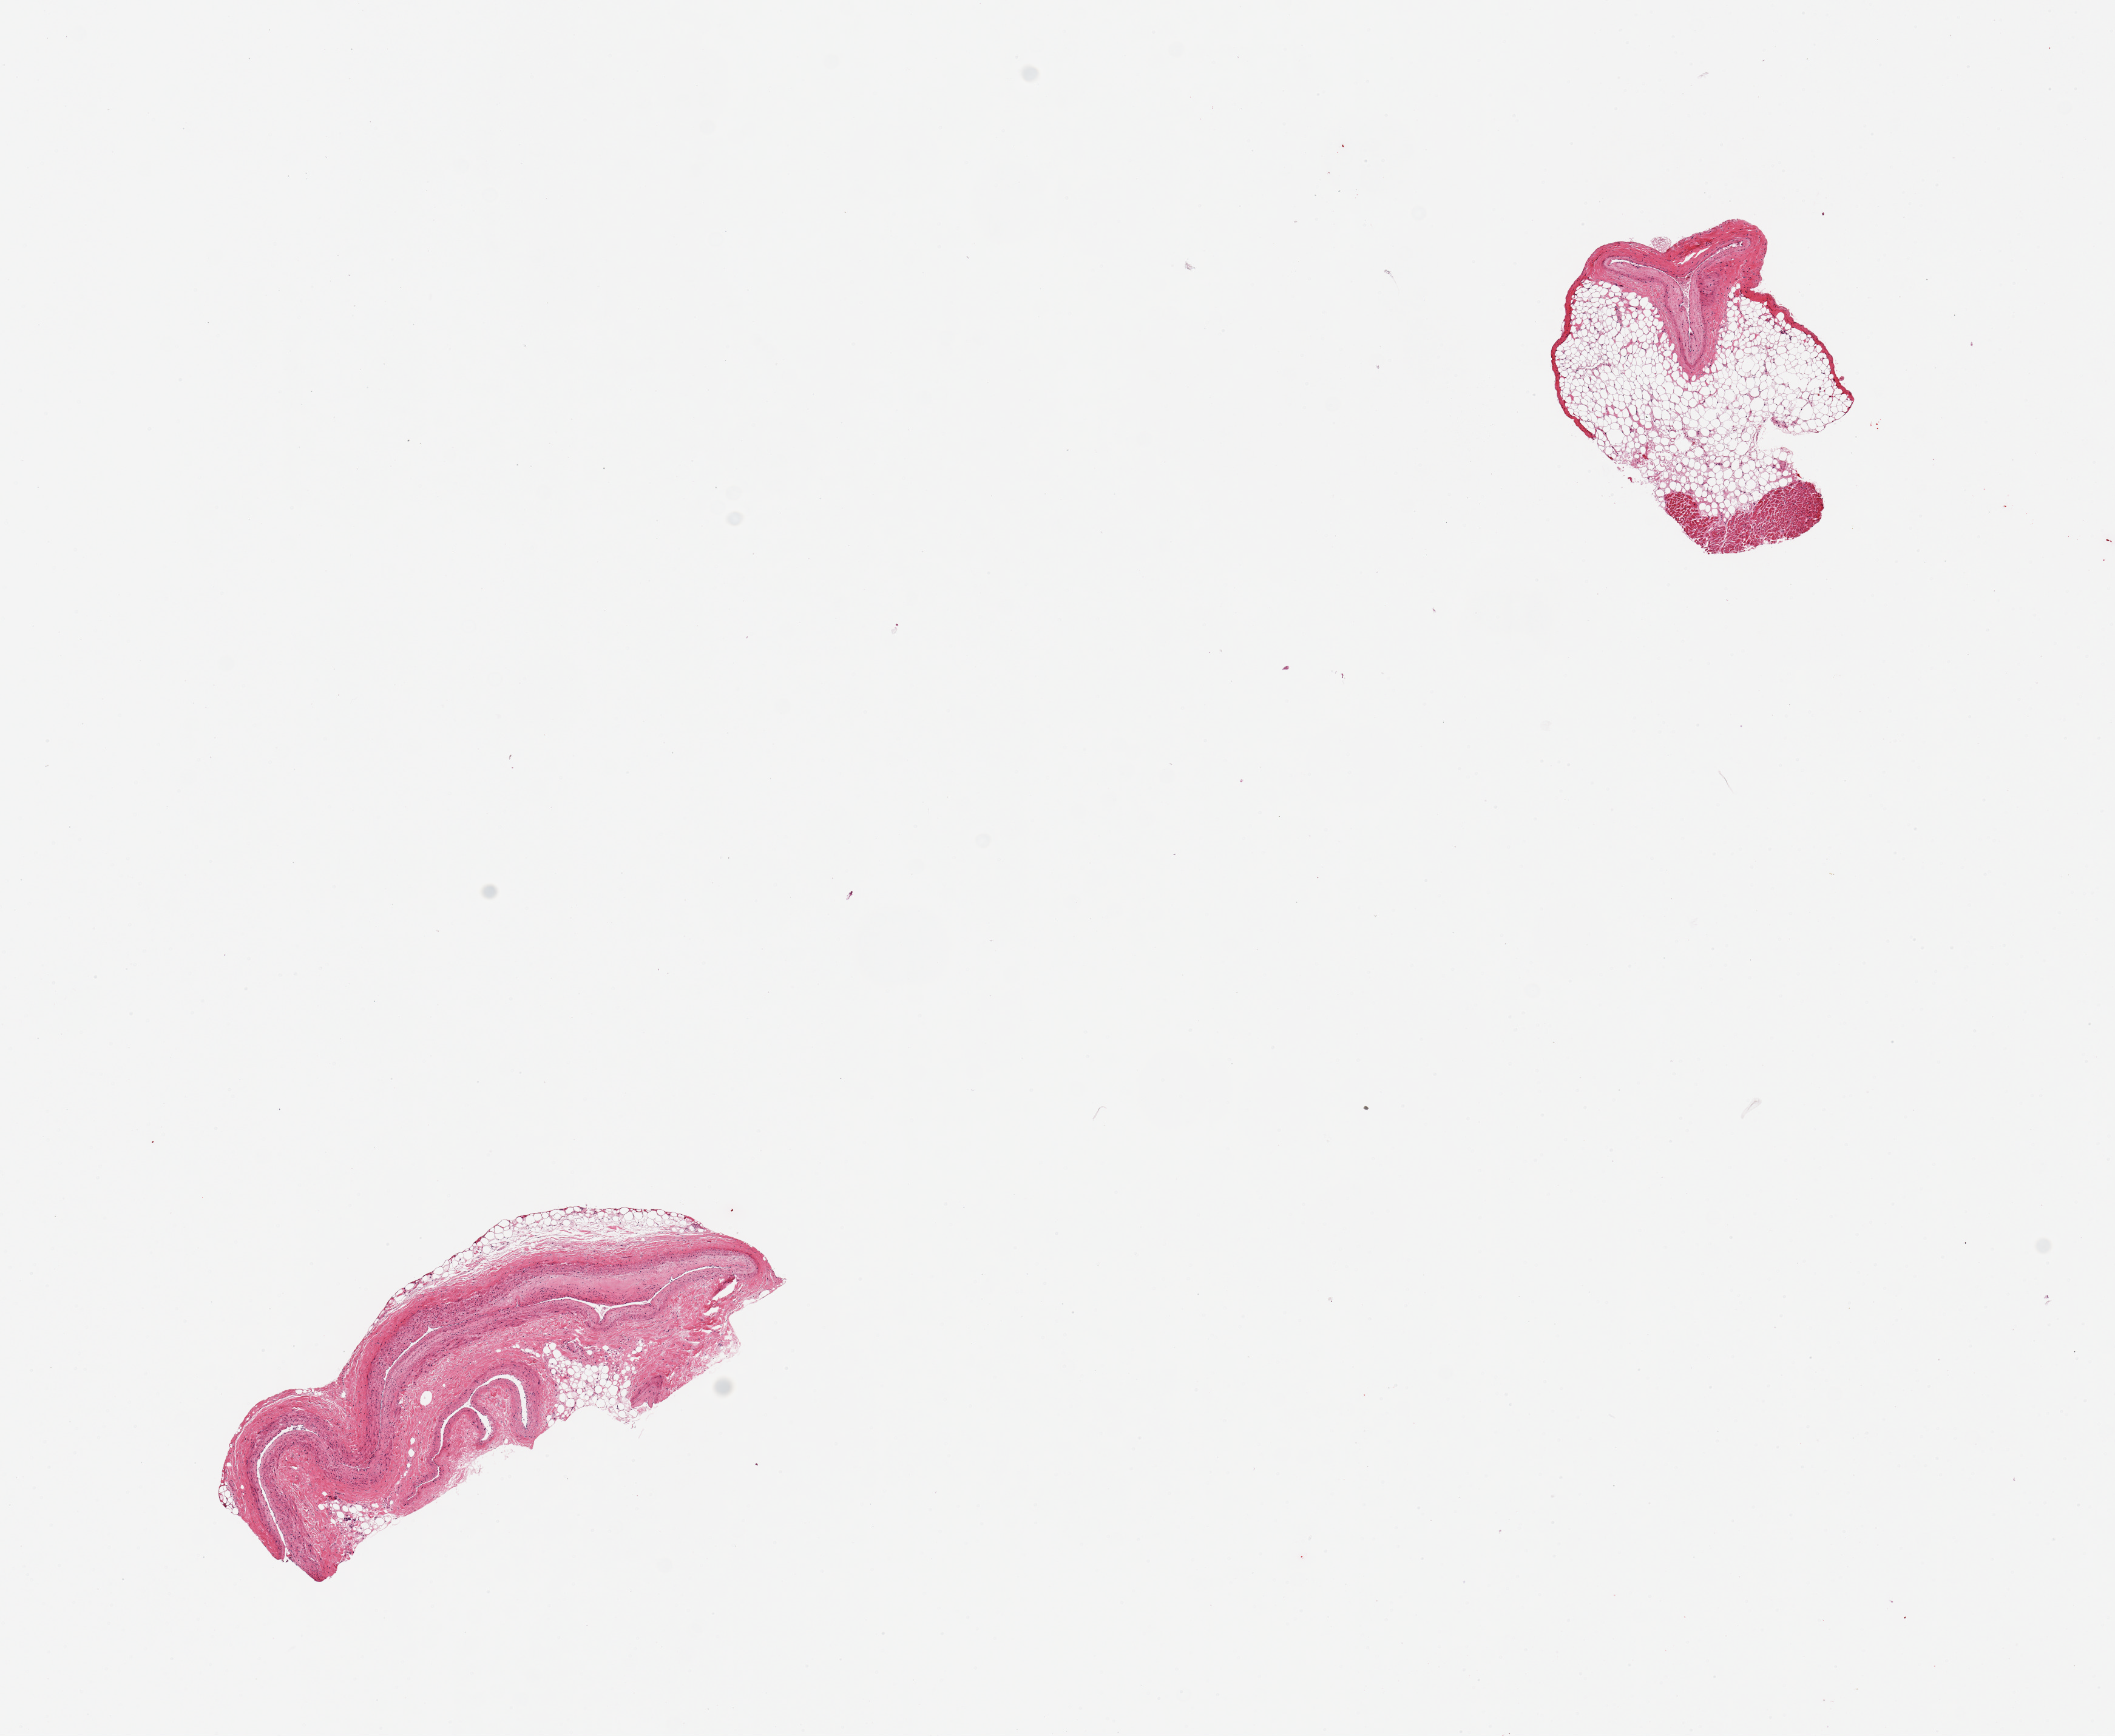
Digitized hematoxylin and eosin (H&E)-stained section, a low-resolution overview of the entire scanned area, about 13.8 x 11.3 mm; PAXgene-fixed, paraffin-embedded tissue; sampled site (target tissue): coronary artery; tissue donor sample. Female donor.
Reviewer comment on this tissue sample: 2 pieces, one all vessel with minute adherent fat; one is 80% fat with minute section of vessel.